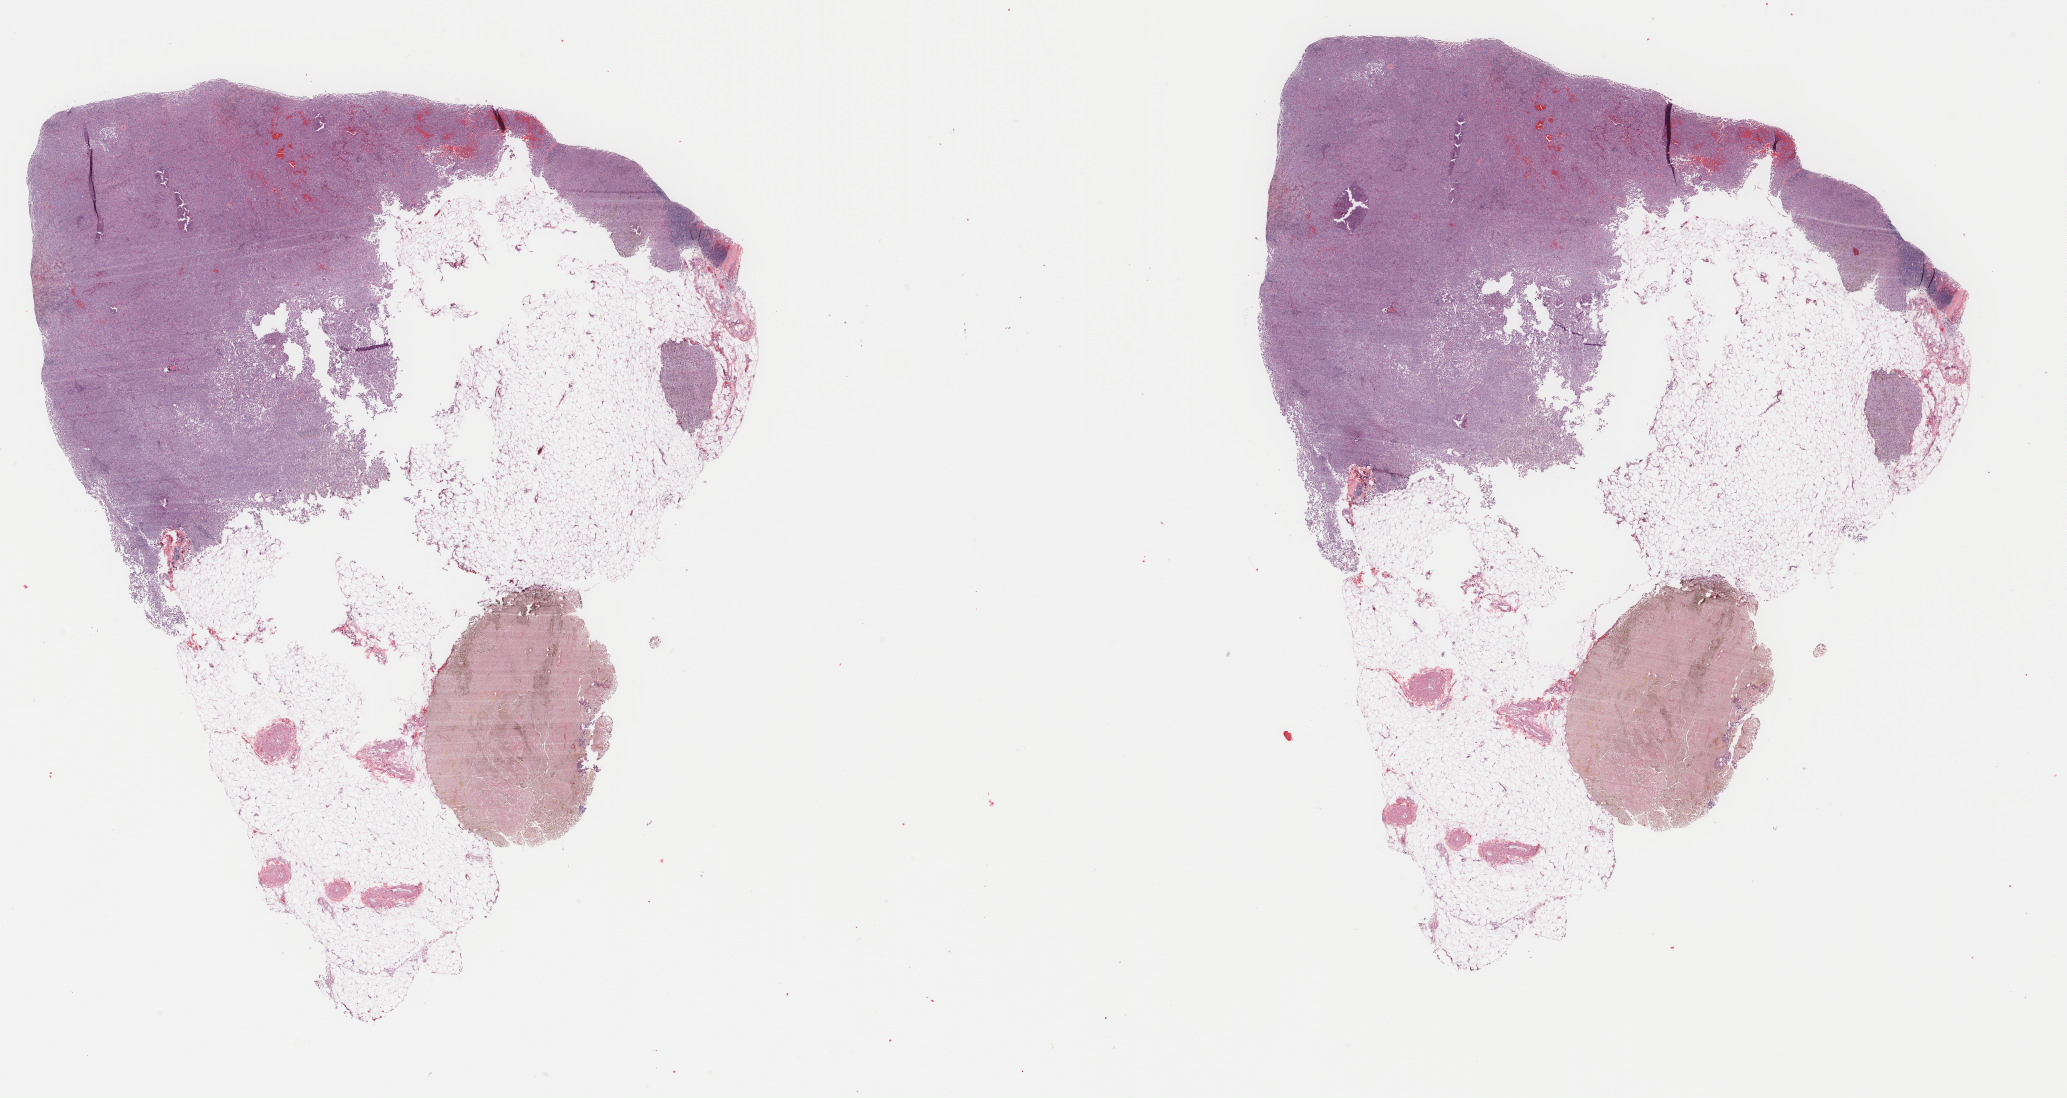
H&E-stained whole-slide image, low-resolution overview of the scanned area, about 32.8 x 17.4 mm (acquisition: 40x scan); formalin-fixed paraffin-embedded (FFPE) diagnostic section; skin, primary tumour sample. Patient: male, age at initial diagnosis 44 years.
- diagnosis: Malignant melanoma, NOS